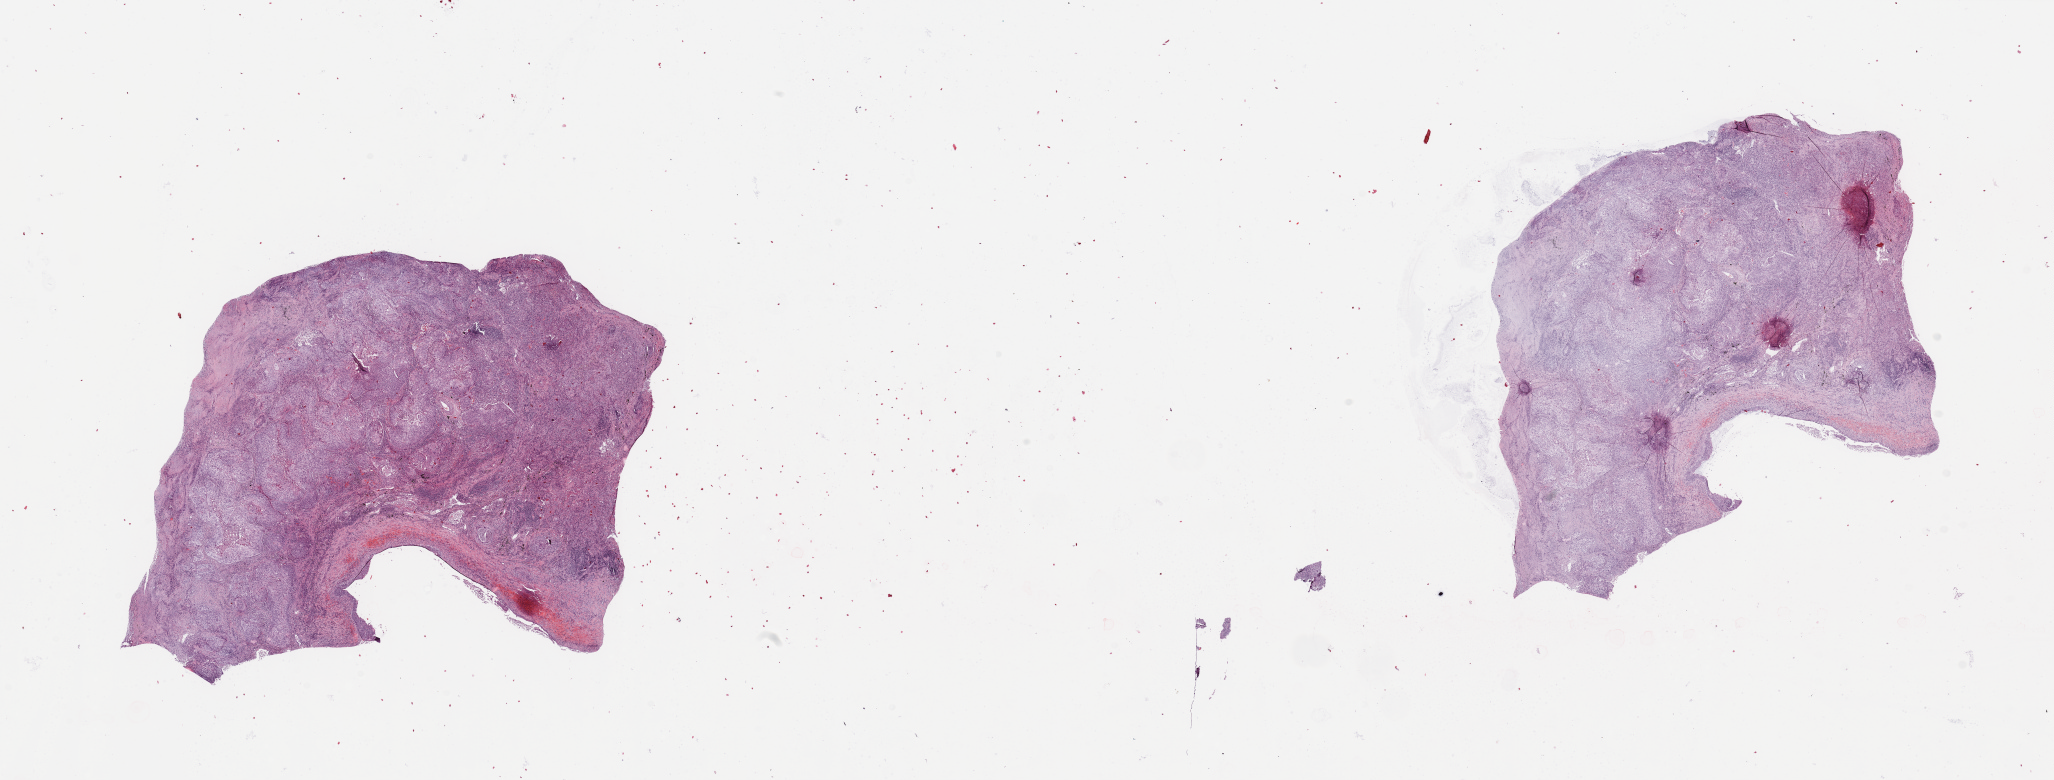
Whole-slide histology image, H&E — shown as a low-resolution overview of the whole scanned area (about 32.5 x 12.3 mm, from a 20x scan), tumour tissue sample, lung. Patient: male, age 53 years. Histologic grade: G2 (moderately differentiated).
* AJCC pathologic stage: IIIA
* histologic diagnosis: Squamous cell carcinoma, NOS